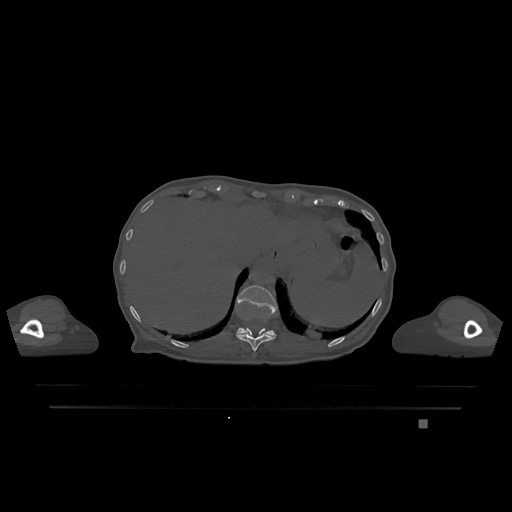
CT including the spine, one axial slice. Position 568 of 1317 along the scan axis. Bone window (W 1800 / L 400 HU). 0.5 mm slice thickness. 512 × 512 image matrix. Patient: female, 74 years. From the clinical record (not read from this slice): primary cancer: lung; vertebrae with lytic lesions (as recorded): T1, T4, T5, T6, L4, L5.
Outlined on this slice (semi-automatically segmented with operator editing):
- T11 vertebra: box from (x=236, y=328) to (x=276, y=352) px
- T12 vertebra: (x=237, y=285)–(x=277, y=337)